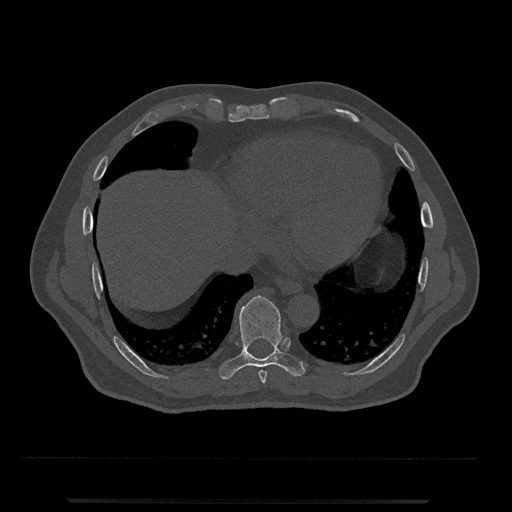
CT including the spine, one axial slice. Position 582 of 797 along the scan axis. Reconstruction kernel Br40s/3. Bone window (W 1800 / L 400 HU). 0.5 mm slice thickness. 512 × 512 image matrix, field of view 419 × 419 mm. Male patient, age 63 years. From the clinical record (not read from this slice): primary cancer: prostate.
Outlined on this slice (semi-automatically segmented with operator editing):
- T8 vertebra: bounding box <258,370,267,383> (left, top, right, bottom; pixels)
- T9 vertebra: <219,296,306,380>